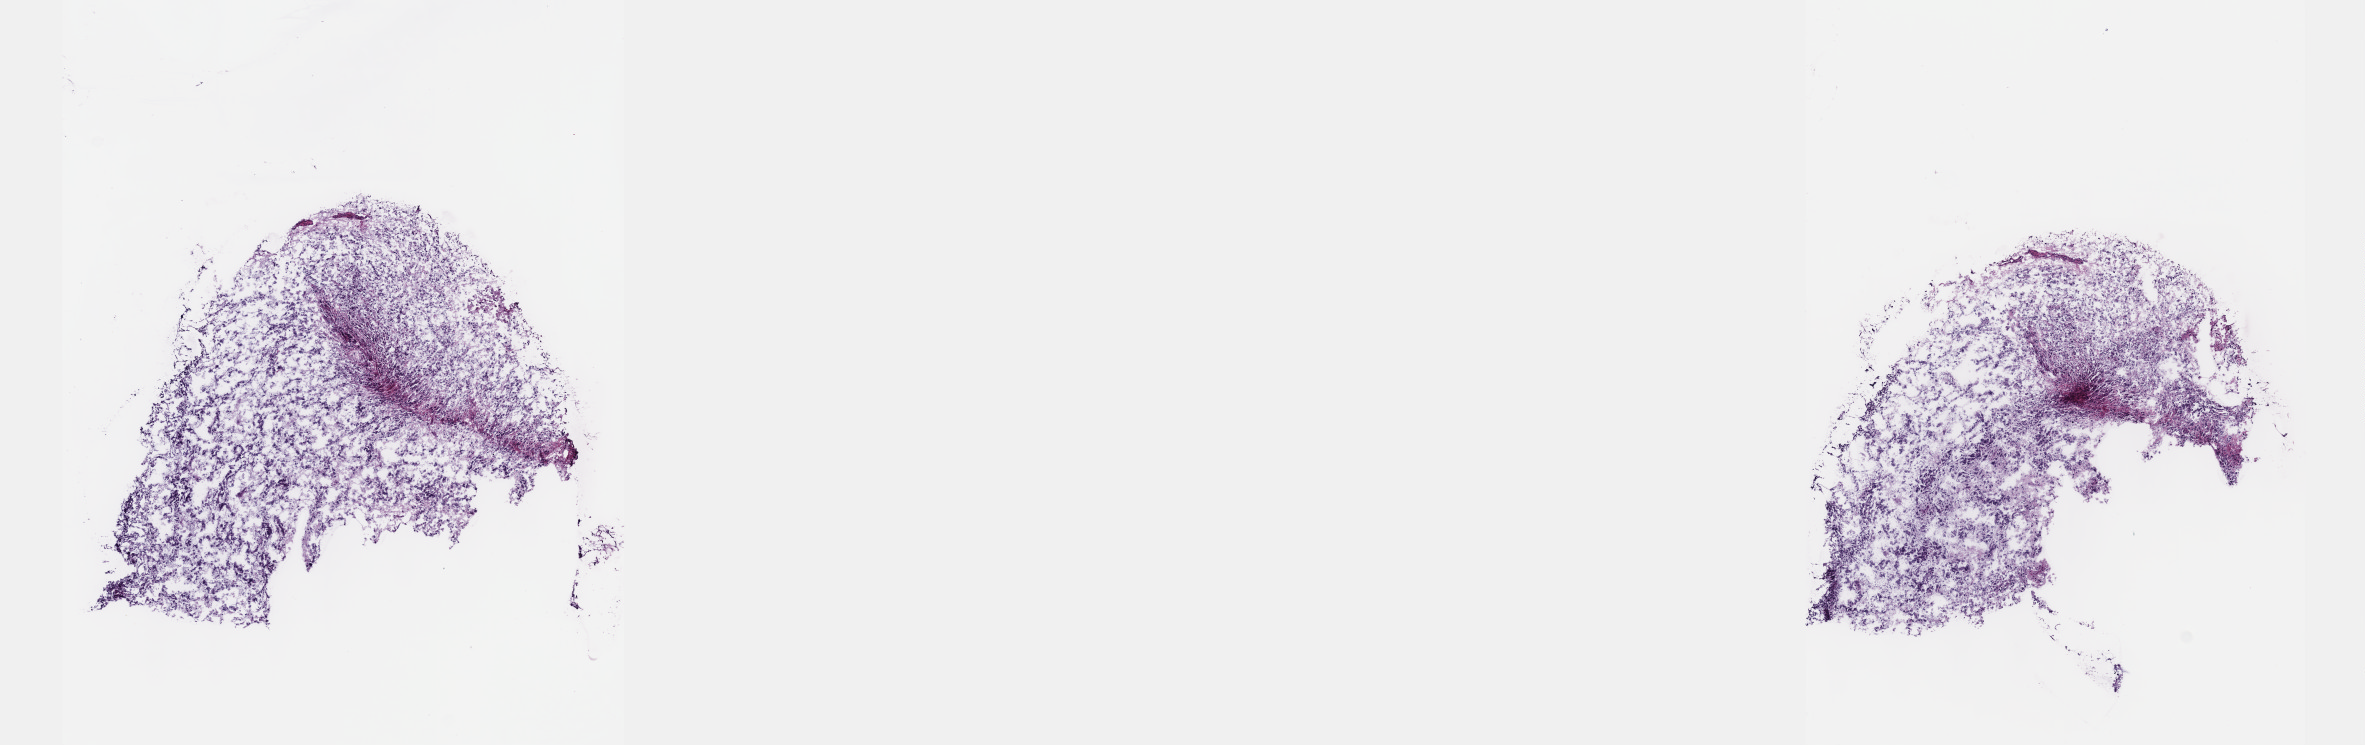
Whole-slide histology image, H&E-stained, a low-resolution overview of the entire scanned area, about 19.1 x 6.0 mm (acquisition: 40x scan); frozen section from the top of the tissue portion; brain, primary tumour sample. Female patient; age at initial diagnosis 44 years. Histologic grade: G3 (poorly differentiated). Composition of this section per pathologist review: tumour cells 50%, tumour nuclei 85%, normal cells 10%, stromal cells 40%, necrosis 0%. Inflammatory infiltration, as recorded: lymphocyte infiltration 0%, monocyte infiltration 0%, neutrophil infiltration 0%.
Diagnosis: Mixed glioma (cerebrum).